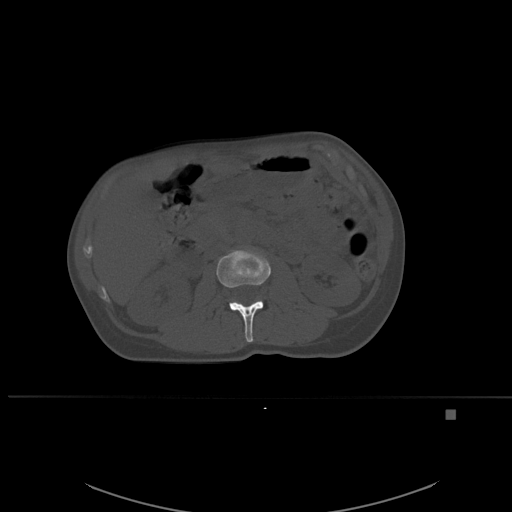
CT including the spine, one axial slice; slice 231 of 537 in the series (ordered by position); bone window (W 1800 / L 400 HU); 1.5 mm slice thickness; 512 × 512 image matrix, field of view 440 × 440 mm. Female patient, age 45 years. Case-level facts recorded for this patient, not image findings: primary cancer: lung.
Annotated regions visible in this slice (semi-automatically segmented with operator editing):
- L2 vertebra: bounding box <216,249,271,342> (left, top, right, bottom; pixels)